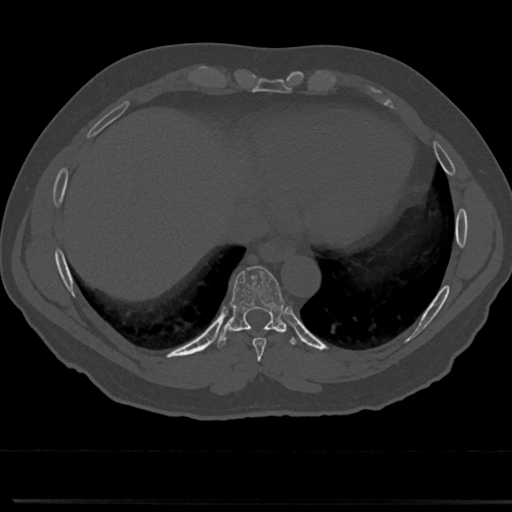
CT including the spine, one axial slice; position 321 of 817 along the scan axis; reconstruction kernel Br40s/3; bone window (W 1800 / L 400 HU); 0.5 mm slice thickness; 512 × 512 image matrix, field of view 355 × 355 mm. Male patient, age 61 years. From the clinical record (not read from this slice): primary cancer: prostate.
Outlined on this slice (semi-automatic segmentation, software-assisted and operator-edited):
- T7 vertebra: bounding box <258,361,266,376> (left, top, right, bottom; pixels)
- T8 vertebra: <215,268,307,356>